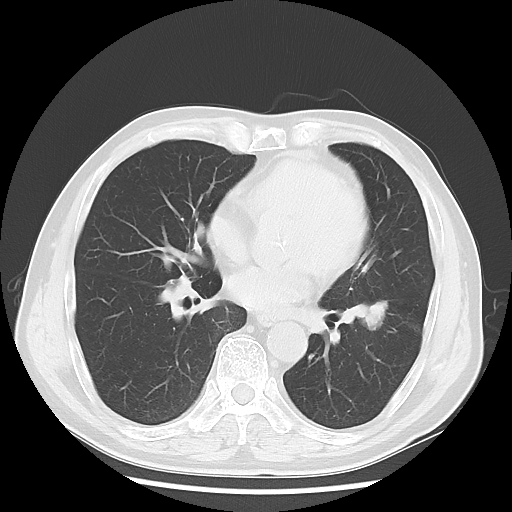
Chest CT, one axial slice. Slice 30 of 68 in the series (ordered by position). 120 kVp. Lung window (W 1500 / L -600 HU). 5 mm slice thickness. 512 × 512 image matrix. Male patient, age 71 years. From the clinical record (not read from this slice): clinical TNM (as recorded): T1c N1 M0; histopathological grade: G2-3.
Annotated regions visible in this slice (bounding box drawn by a radiologist):
- lung tumour (recorded histology: adenocarcinoma): box from (x=350, y=292) to (x=388, y=344) px